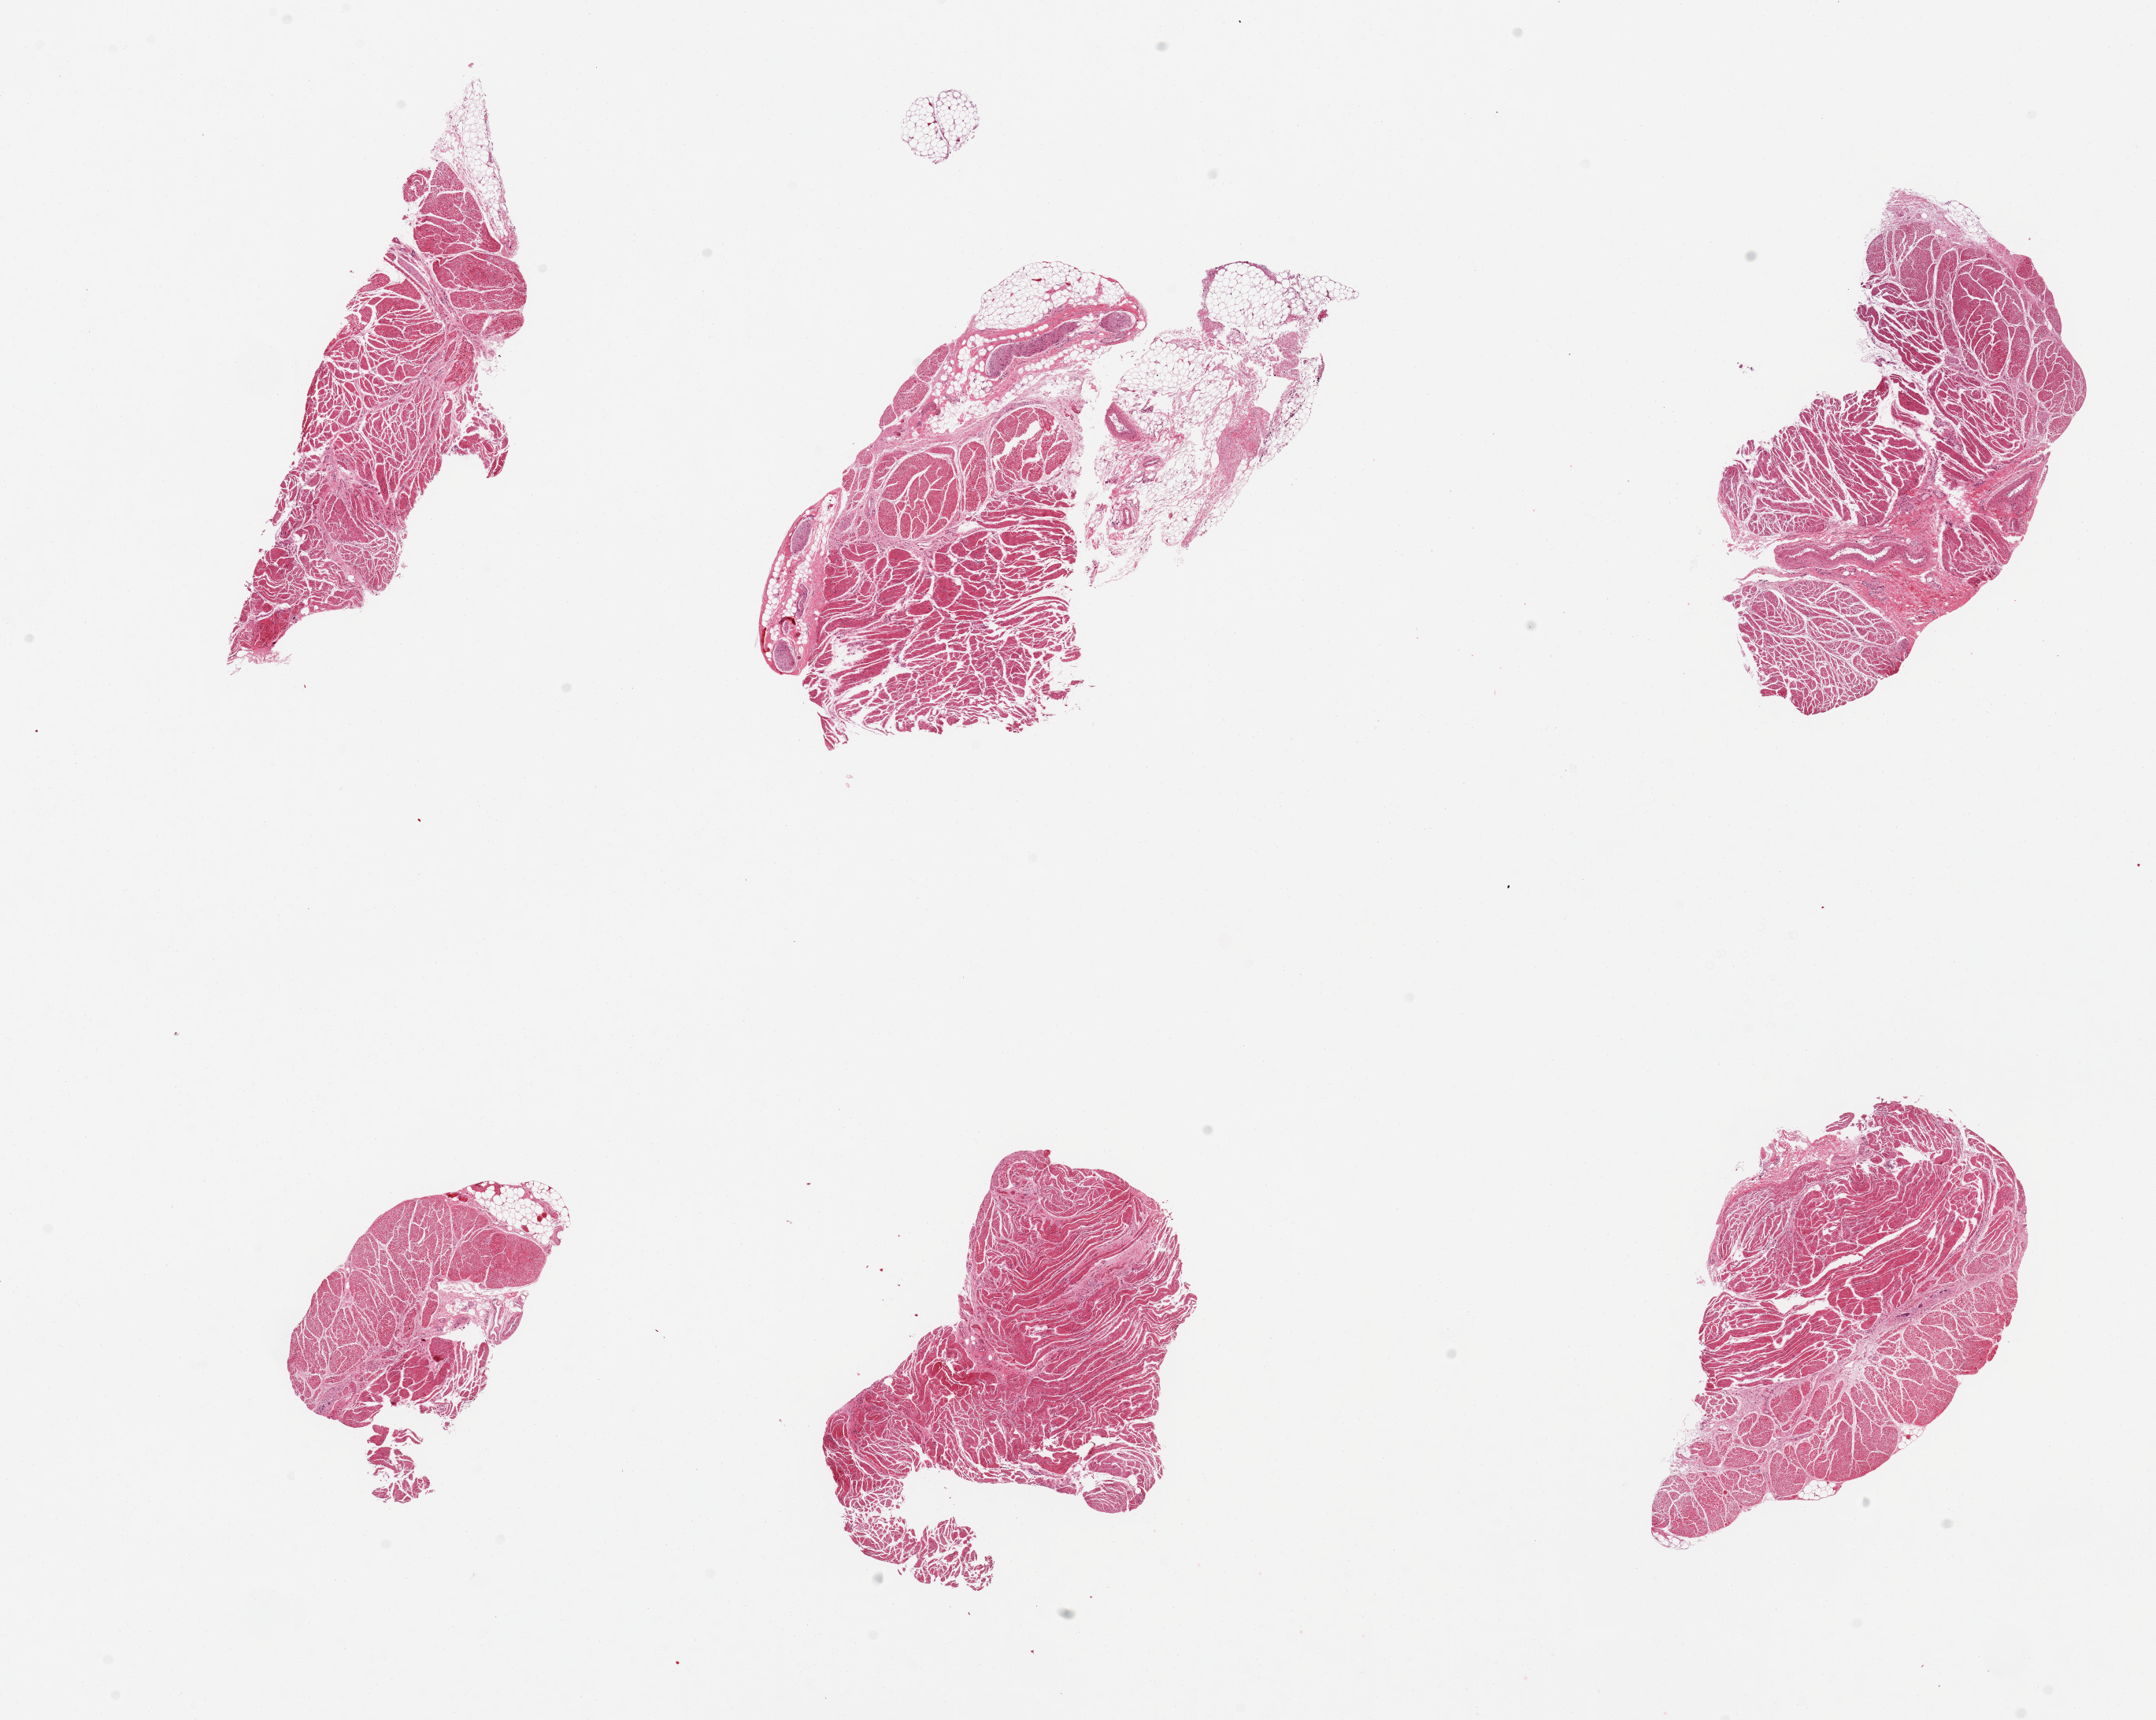
Whole-slide image, haematoxylin and eosin stain, whole scanned area (about 21.7 x 17.3 mm) shown as a low-resolution overview; PAXgene-fixed, paraffin-embedded tissue; target tissue: gastroesophageal junction; tissue donor sample. Donor sex: male.
Pathologist's review note for this sample: 6 pieces, all target muscularis, nubbin of adherent fat.